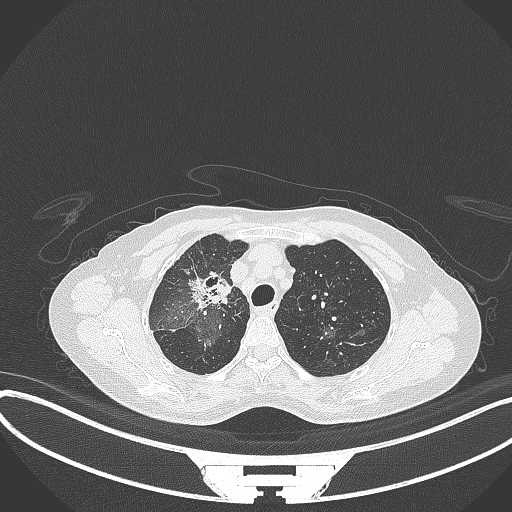
Chest CT, one axial slice. Slice 248 of 284 in the series (ordered by position). Reconstruction kernel B70f. 120 kVp. Lung window (W 1500 / L -600 HU). 512 × 512 image matrix. Patient: female, 59 years. Case-level facts recorded for this patient, not image findings: clinical TNM (as recorded): T3 N0 M0.
Outlined on this slice (bounding box drawn by a radiologist):
- lung tumour (recorded histology: adenocarcinoma): box from (x=185, y=268) to (x=230, y=311) px